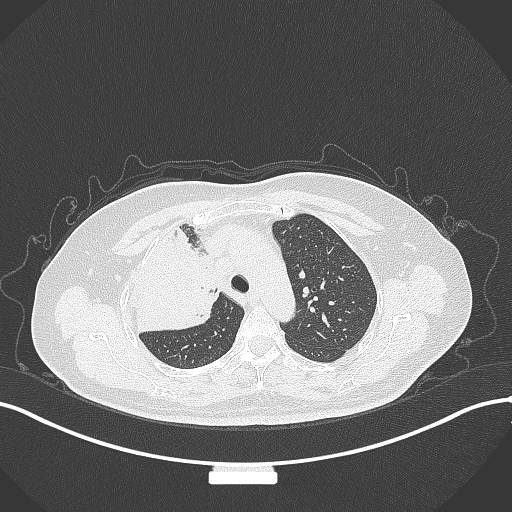
Chest CT, one axial slice; position 230 of 309 along the scan axis; 120 kVp; lung window (W 1500 / L -600 HU); 512 × 512 image matrix, field of view 400 × 400 mm. Patient: female, 60 years. Case-level facts recorded for this patient, not image findings: clinical TNM (as recorded): T3 N1 M1.
Structures marked on this image (rectangle marked by the reading radiologist):
- lung tumour (recorded histology: adenocarcinoma): bounding box <128,218,220,336> (left, top, right, bottom; pixels)